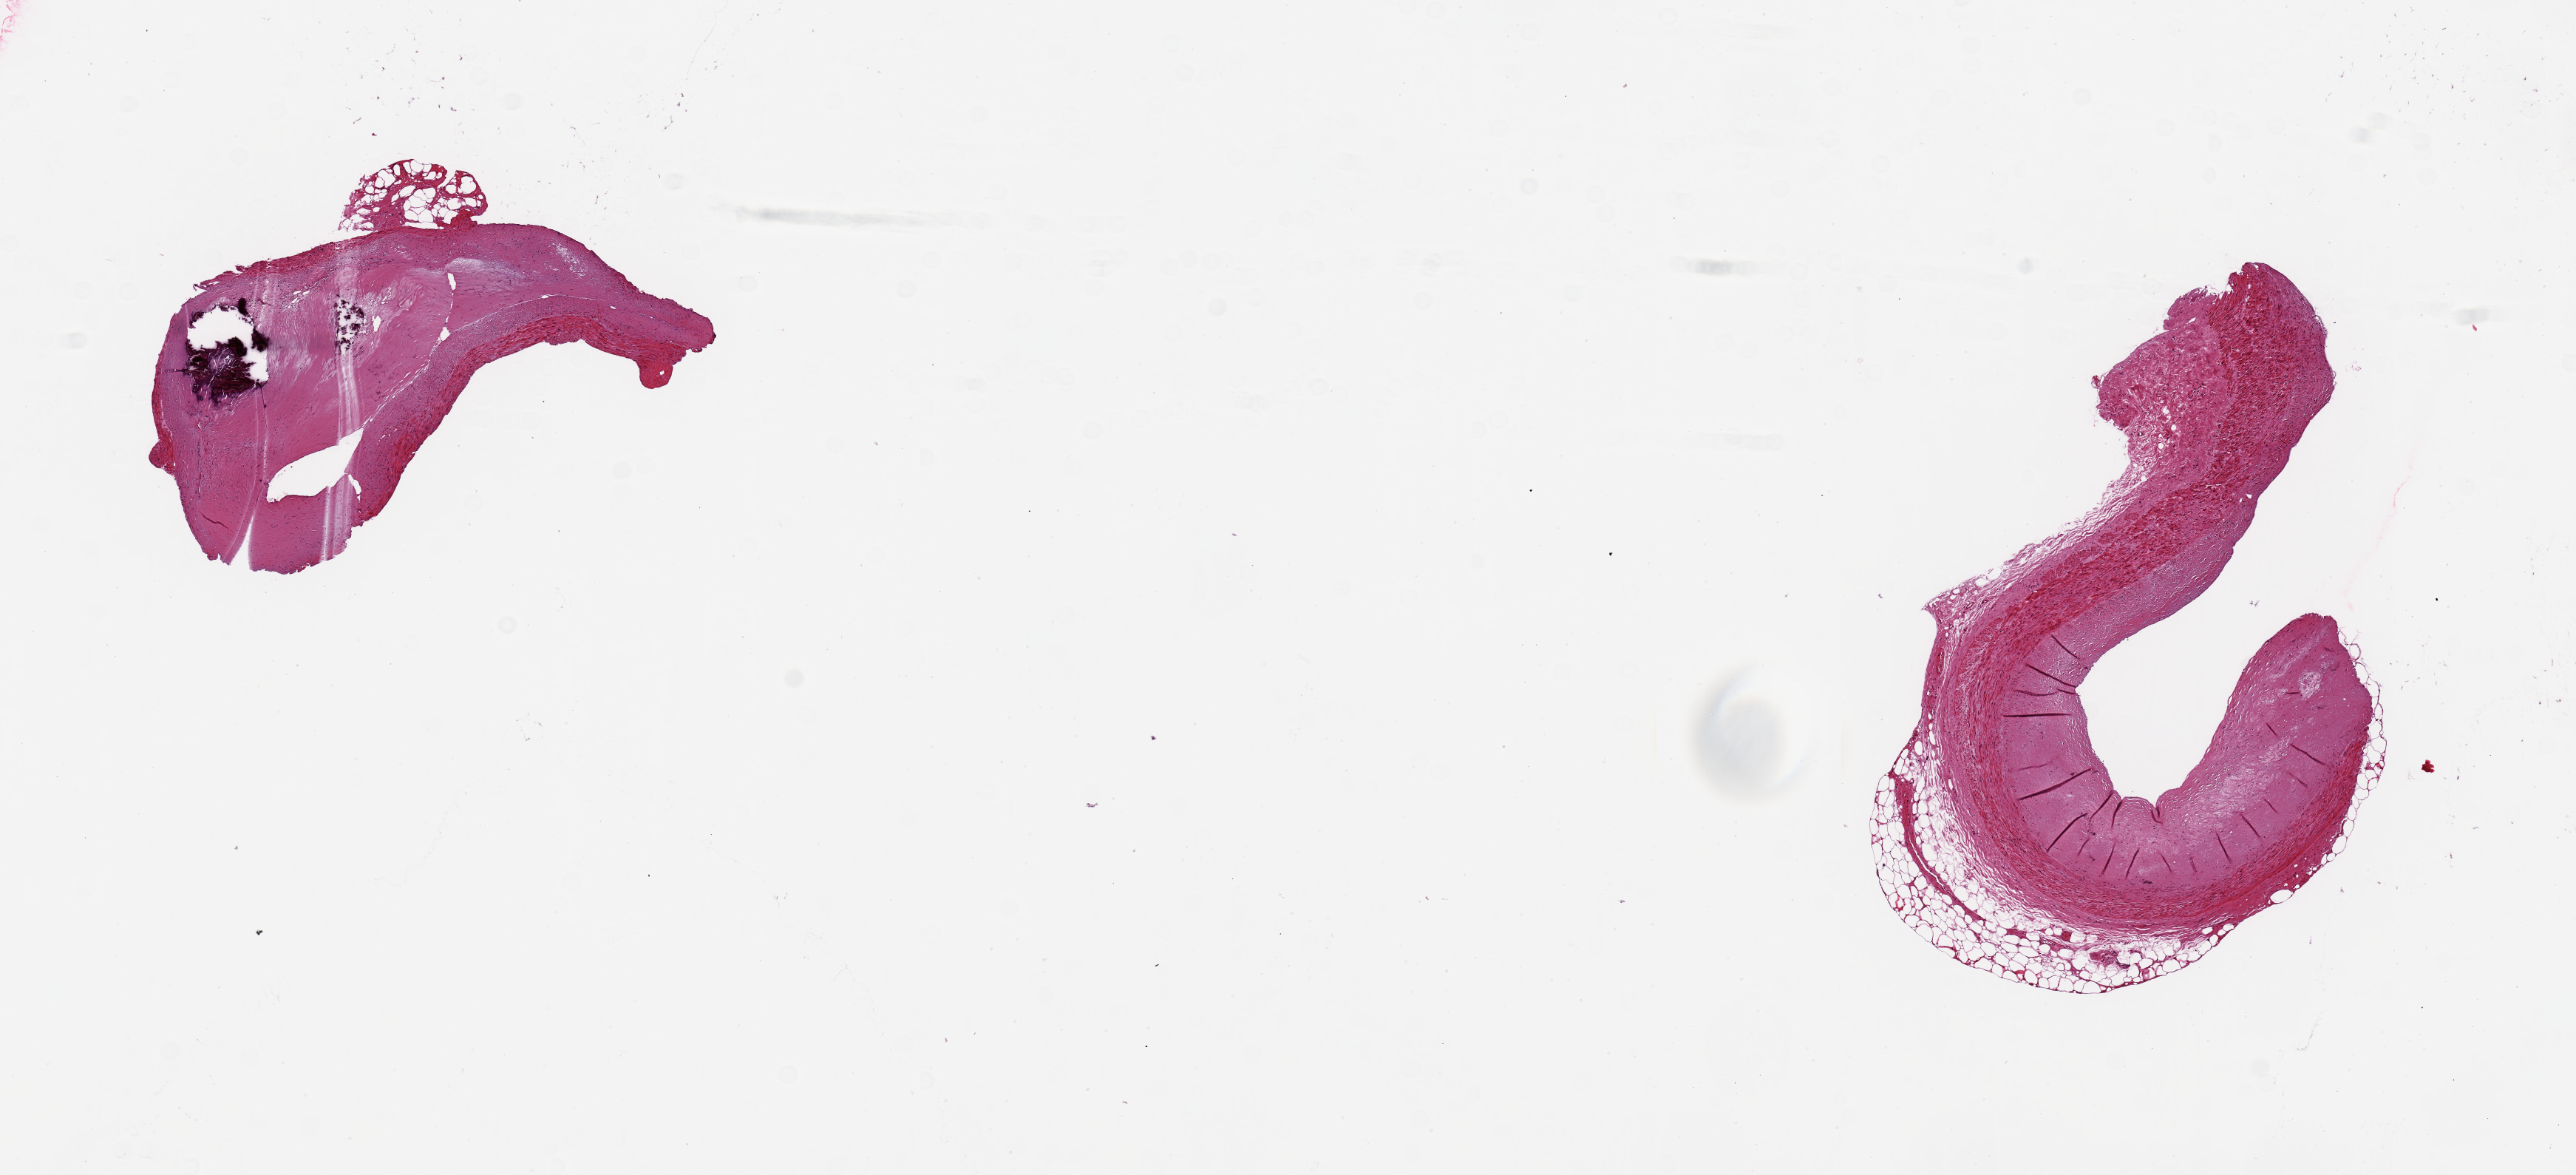
Whole-slide image, hematoxylin and eosin (H&E) stain, brightfield, a low-resolution overview of the entire scanned area, about 13.8 x 6.3 mm; PAXgene-fixed paraffin-embedded (PFPE) section; target tissue: coronary artery; donor tissue sample. Male donor.
Review note (as recorded): 2 pieces, 3x2 & 4x3mm; subtotally occlusive atherosclerosis is present.